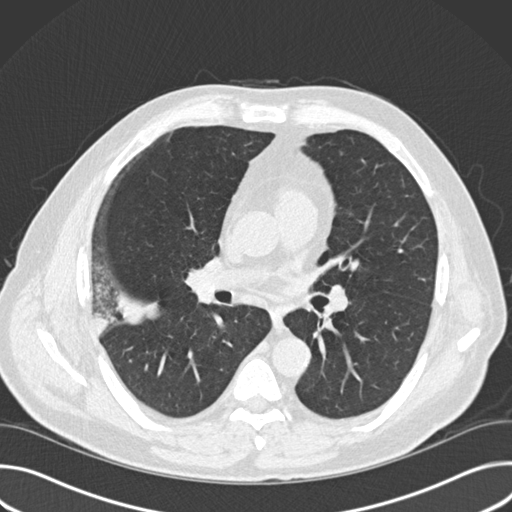
Low-dose screening chest CT, one axial slice; slice 90 of 157 in the series (ordered by position); 120 kVp; lung window (W 1500 / L -600 HU); 2 mm slice thickness; 512 × 512 image matrix, field of view 380 × 380 mm.
Outlined on this slice (manually delineated by an expert):
- lesion 1 (tumor, upper lobe of right lung): bounding box (x1, y1, x2, y2) in pixels: (118, 292, 158, 325)